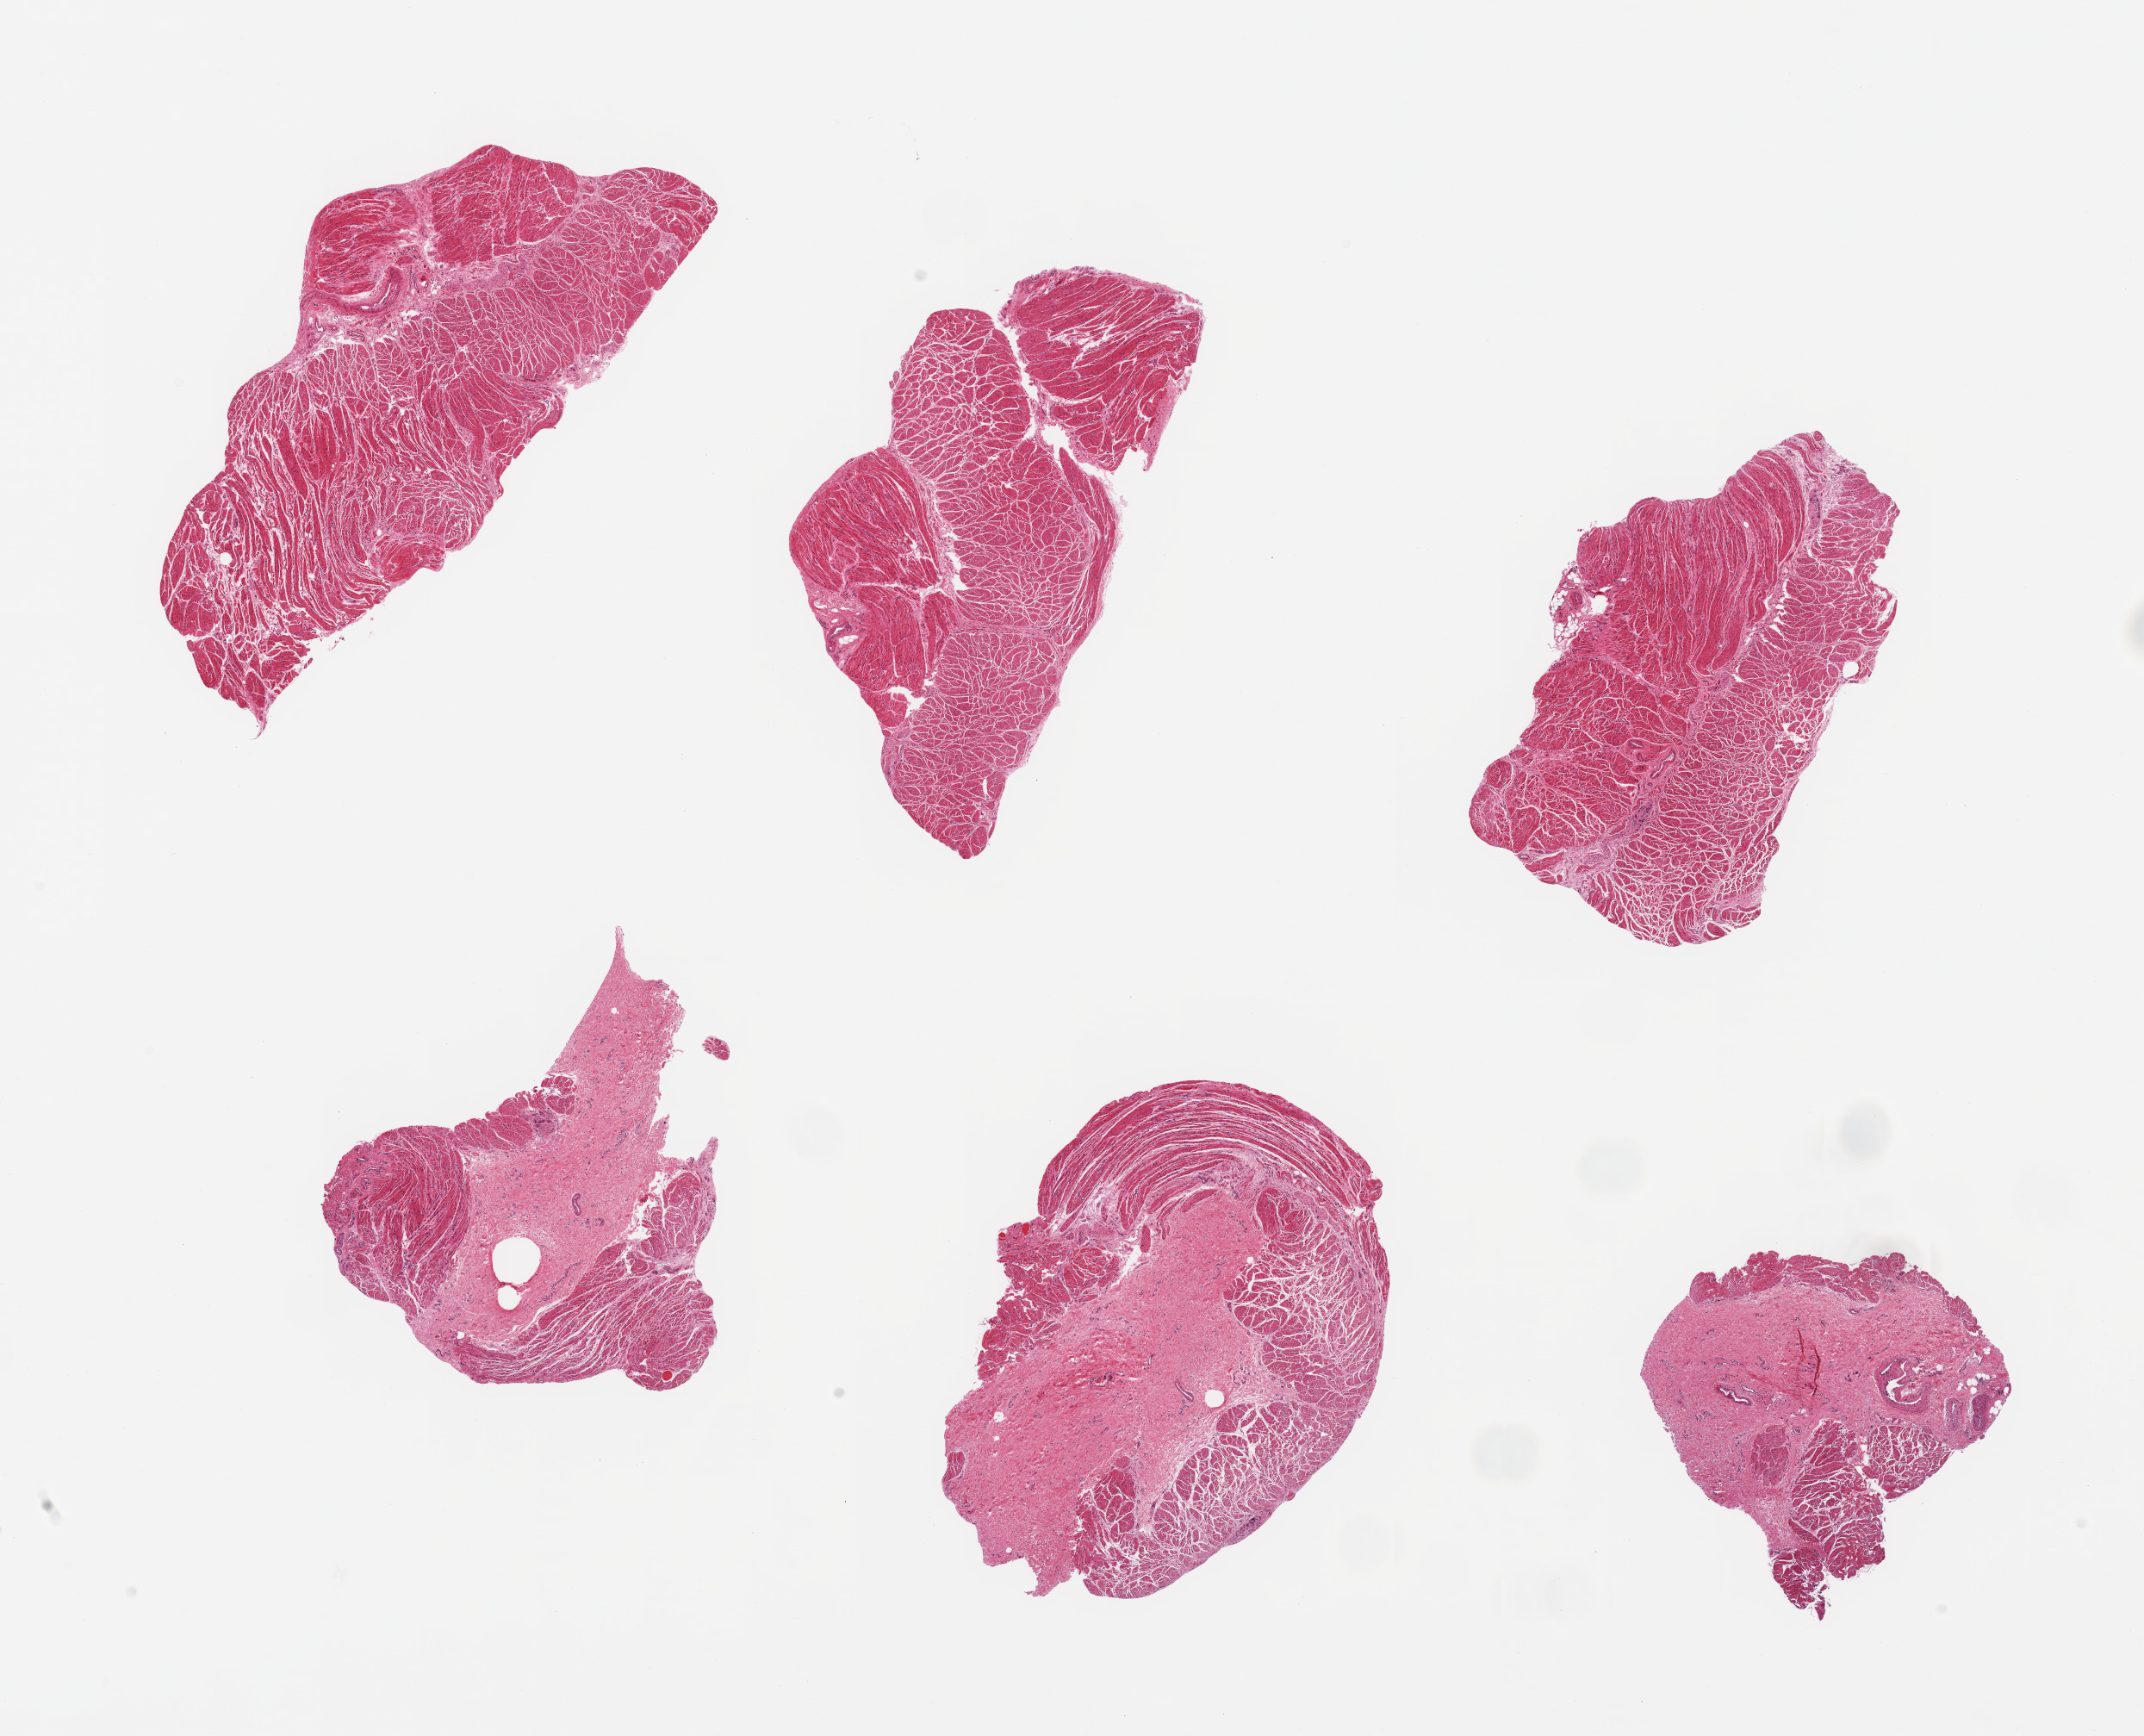
Whole-slide image, H&E stain, brightfield — a low-resolution overview of the entire scanned area, about 19.7 x 15.9 mm, PAXgene-fixed, paraffin-embedded tissue, target tissue: esophageal muscle, tissue donor sample. Female donor.
Pathologist's review note for this sample: 6 pieces; target muscularis and fibrovascular tissue of submucosa.